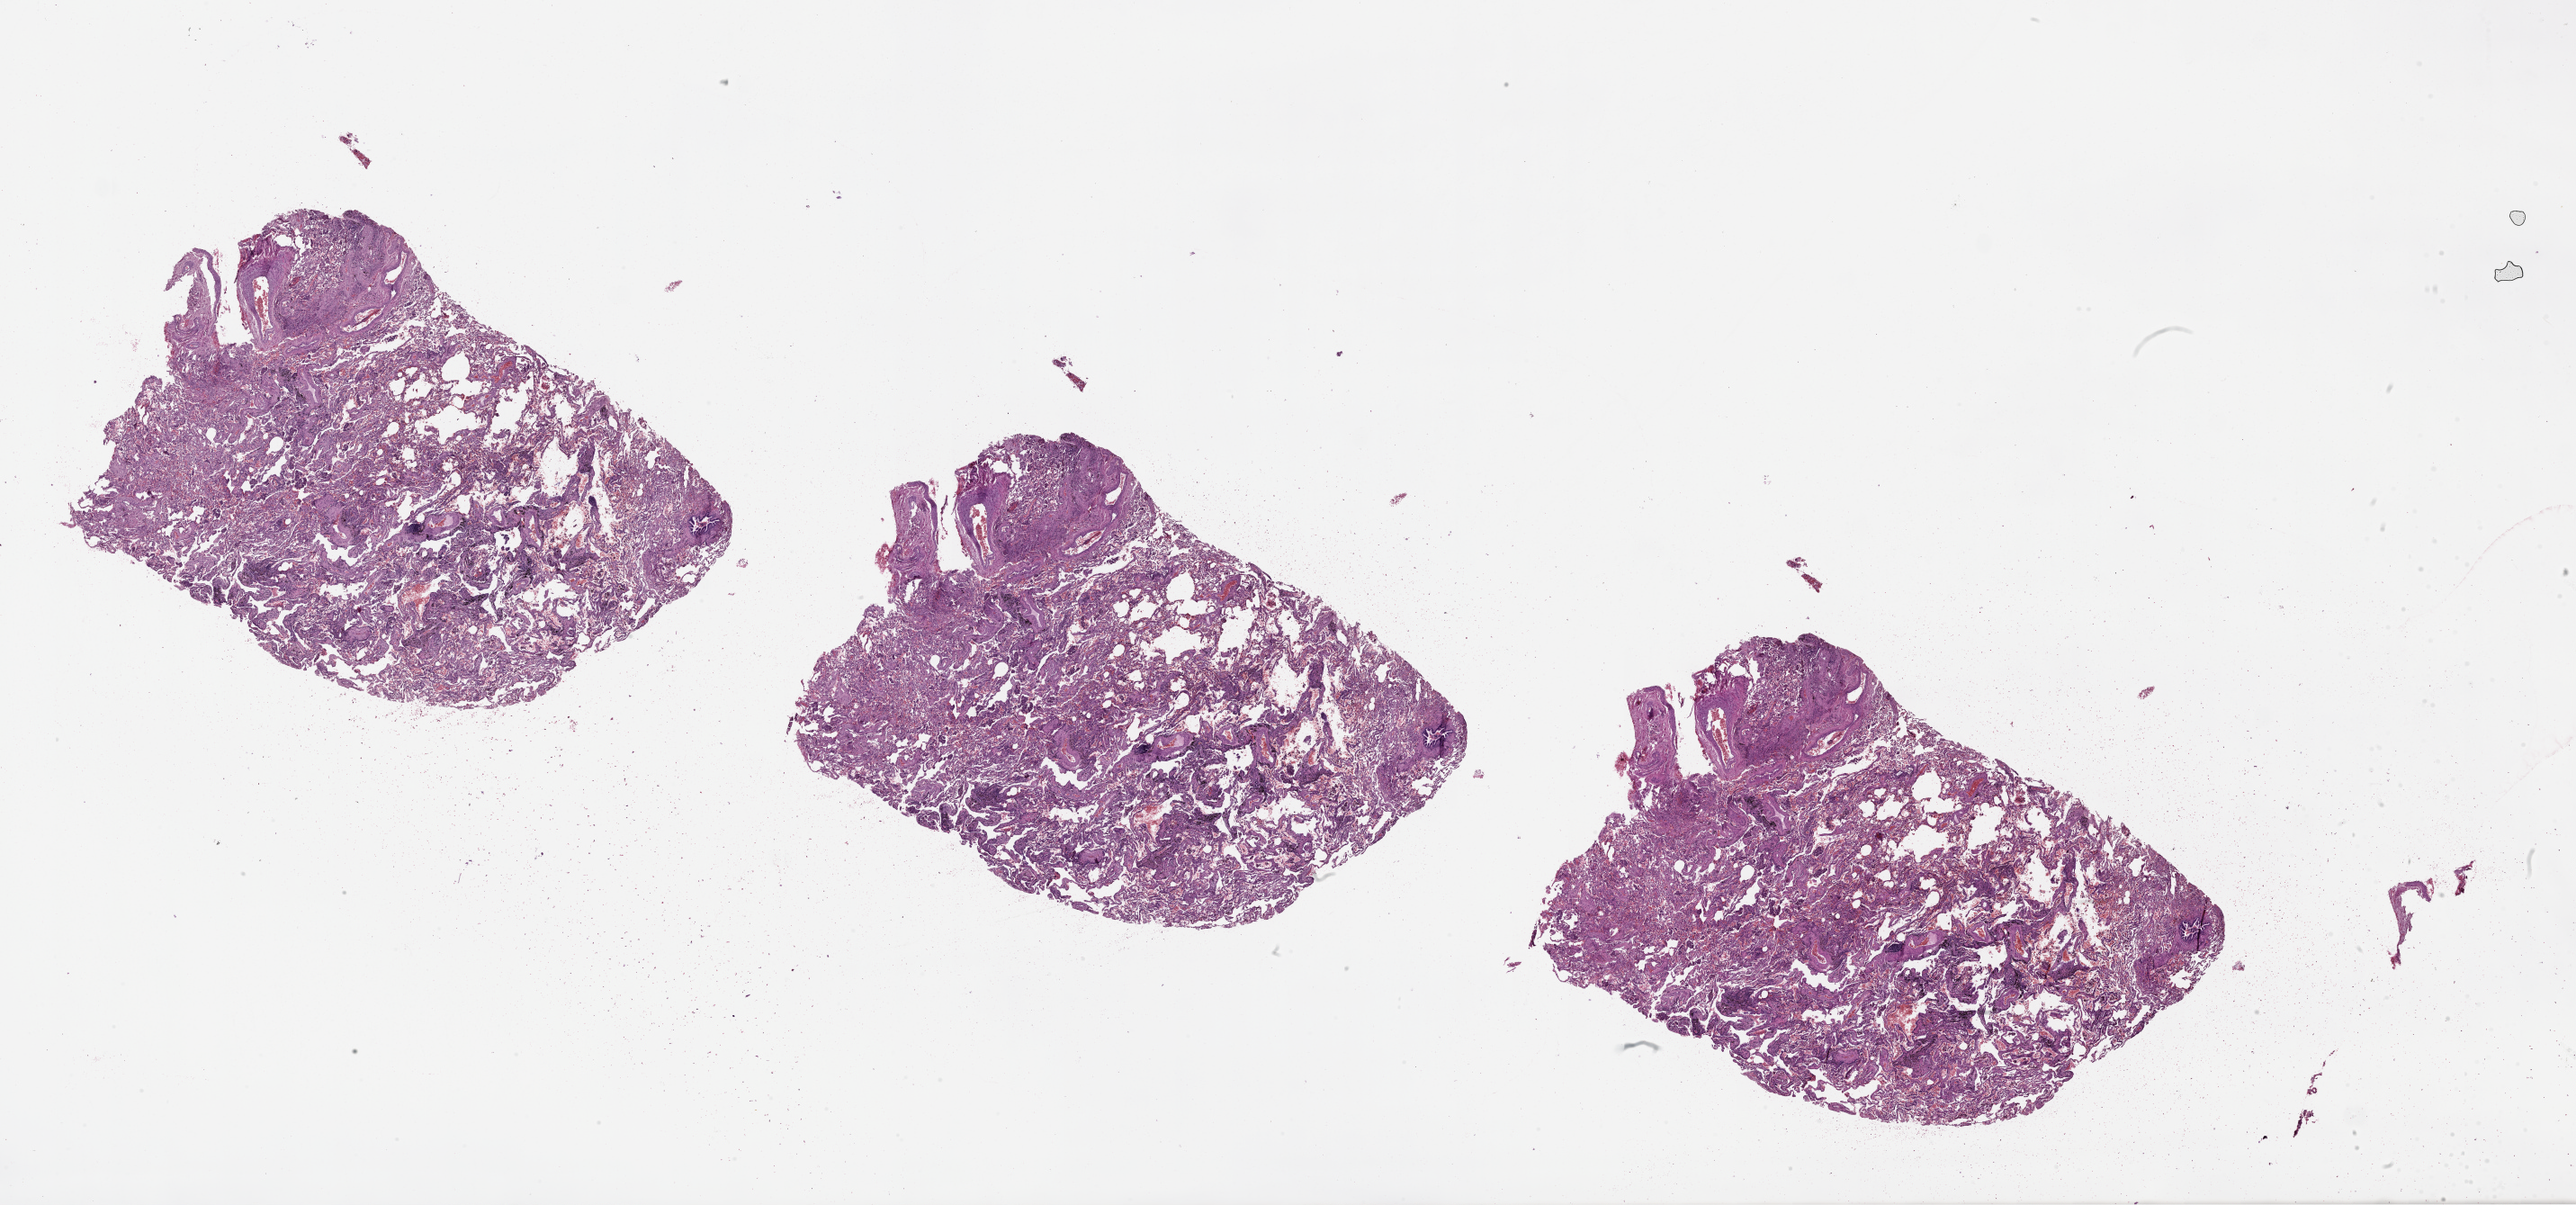
Whole-slide histology image, H&E, a low-resolution overview of the entire scanned area, about 46.1 x 21.6 mm (slide scanned at 20x), normal (non-tumour) tissue sample, lung. Patient: male, age 66 years.
This section: normal (non-tumour) tissue from the same patient. Patient diagnosis (cohort enrolment): squamous cell carcinoma (lung).